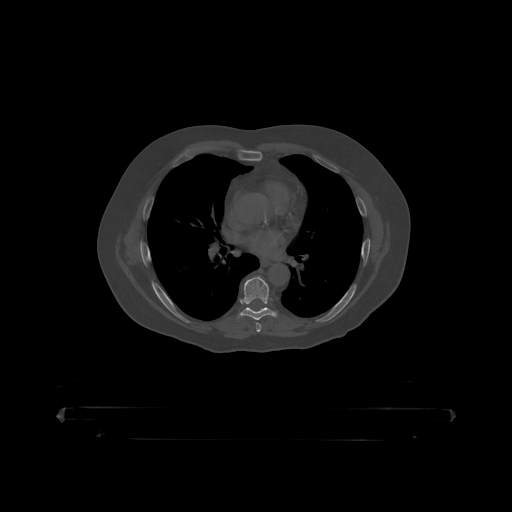
CT including the spine, one axial slice. Slice 280 of 390 in the series (ordered by position). Reconstruction kernel STANDARD. Bone window (W 1800 / L 400 HU). 1.25 mm slice thickness. 512 × 512 image matrix, field of view 650 × 650 mm. Patient: male, 60 years. From the clinical record (not read from this slice): primary cancer: prostate.
Structures marked on this image (semi-automatic segmentation, software-assisted and operator-edited):
- T7 vertebra: bounding box (x1, y1, x2, y2) in pixels: (239, 277, 278, 319)